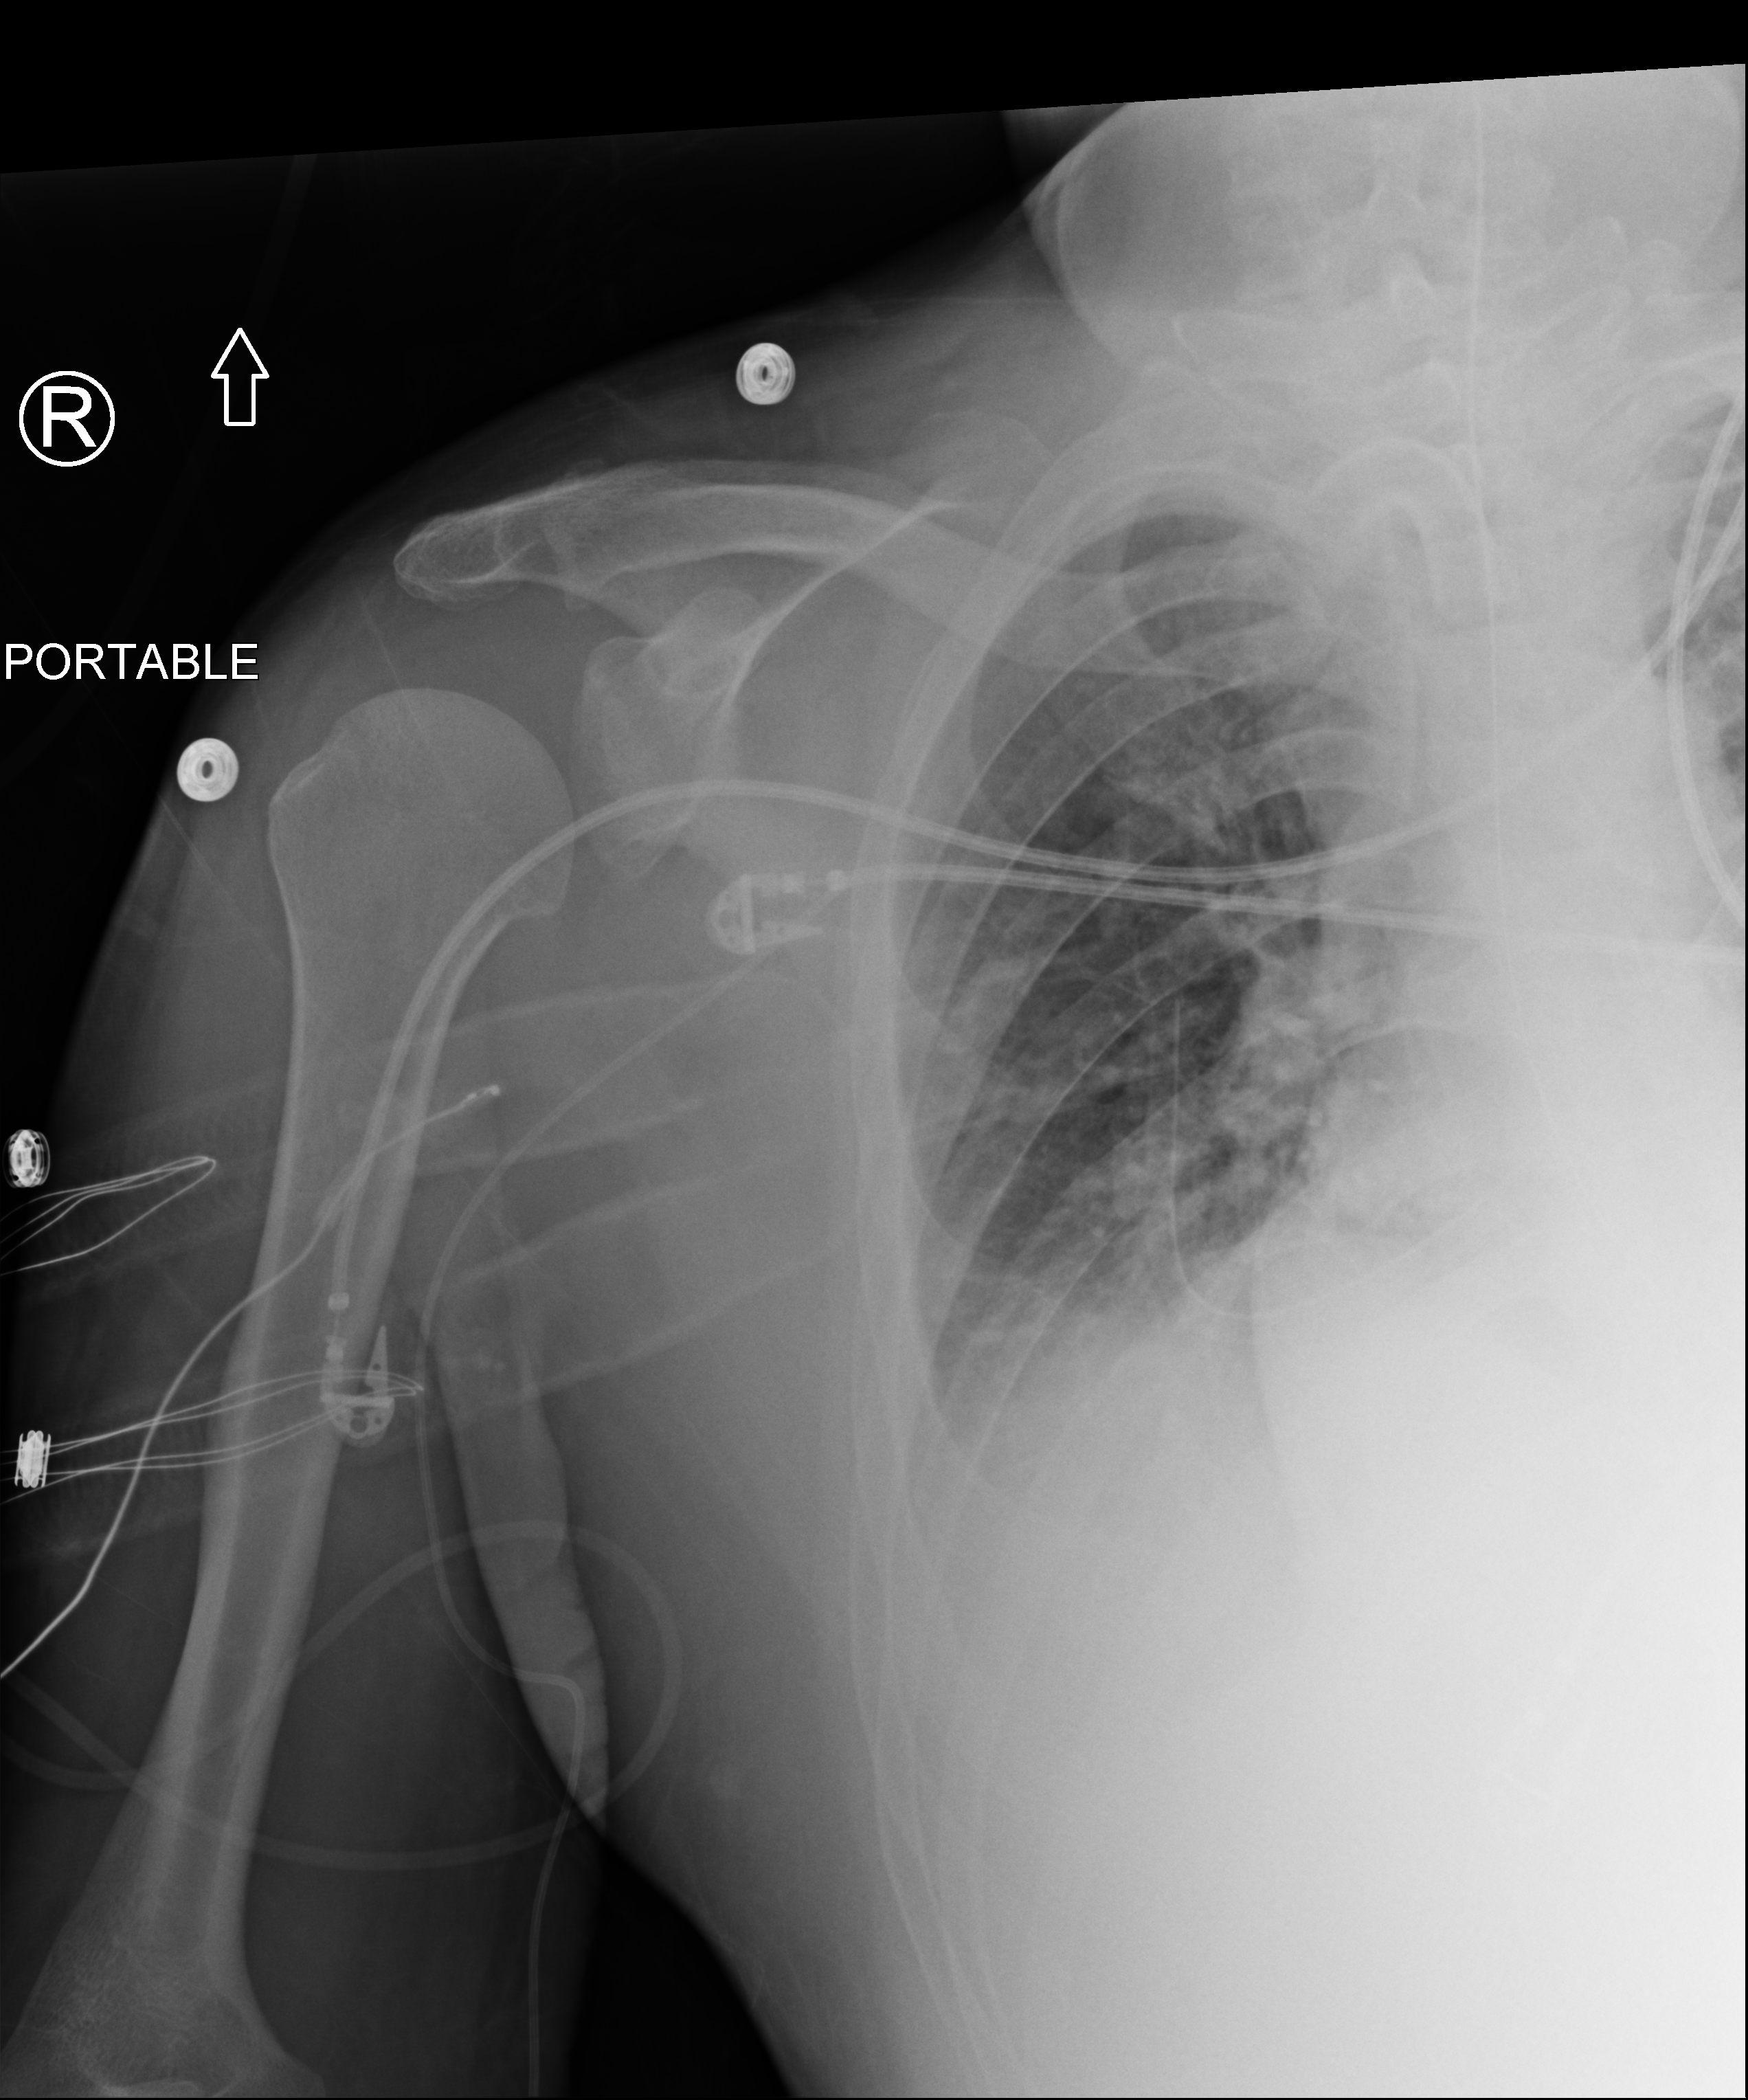
Bedside chest radiograph (computed radiography). Male patient hospitalised with COVID-19, age 18–59 years.
Hospital-stay facts (about this admission, not read from this image; timing relative to this image not recorded): mechanically ventilated during this hospital stay: yes.